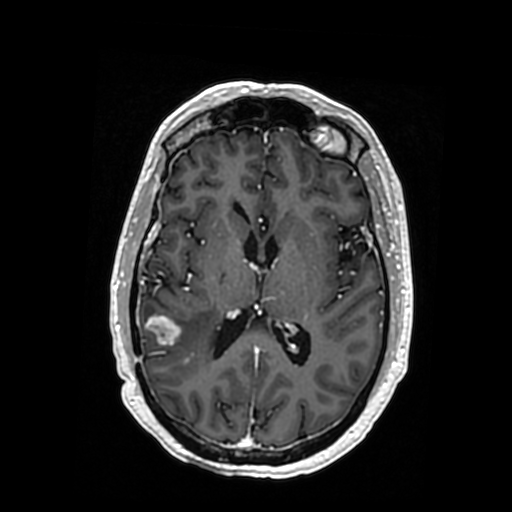
Brain MRI from a brain-tumour surgery series, one axial slice. Slice 172 of 364 in the series (ordered by position). T1-weighted post-contrast. 0.5 mm slice thickness. 512 × 512 image matrix, field of view 260 × 260 mm. From the clinical record (not read from this slice): histopathology: Oligodendroglioma; WHO grade: 3; IDH mutation: yes.
Structures marked on this image (outlined manually by an expert reader):
- tumour: bounding box [x1, y1, x2, y2] px = [146, 315, 217, 372]